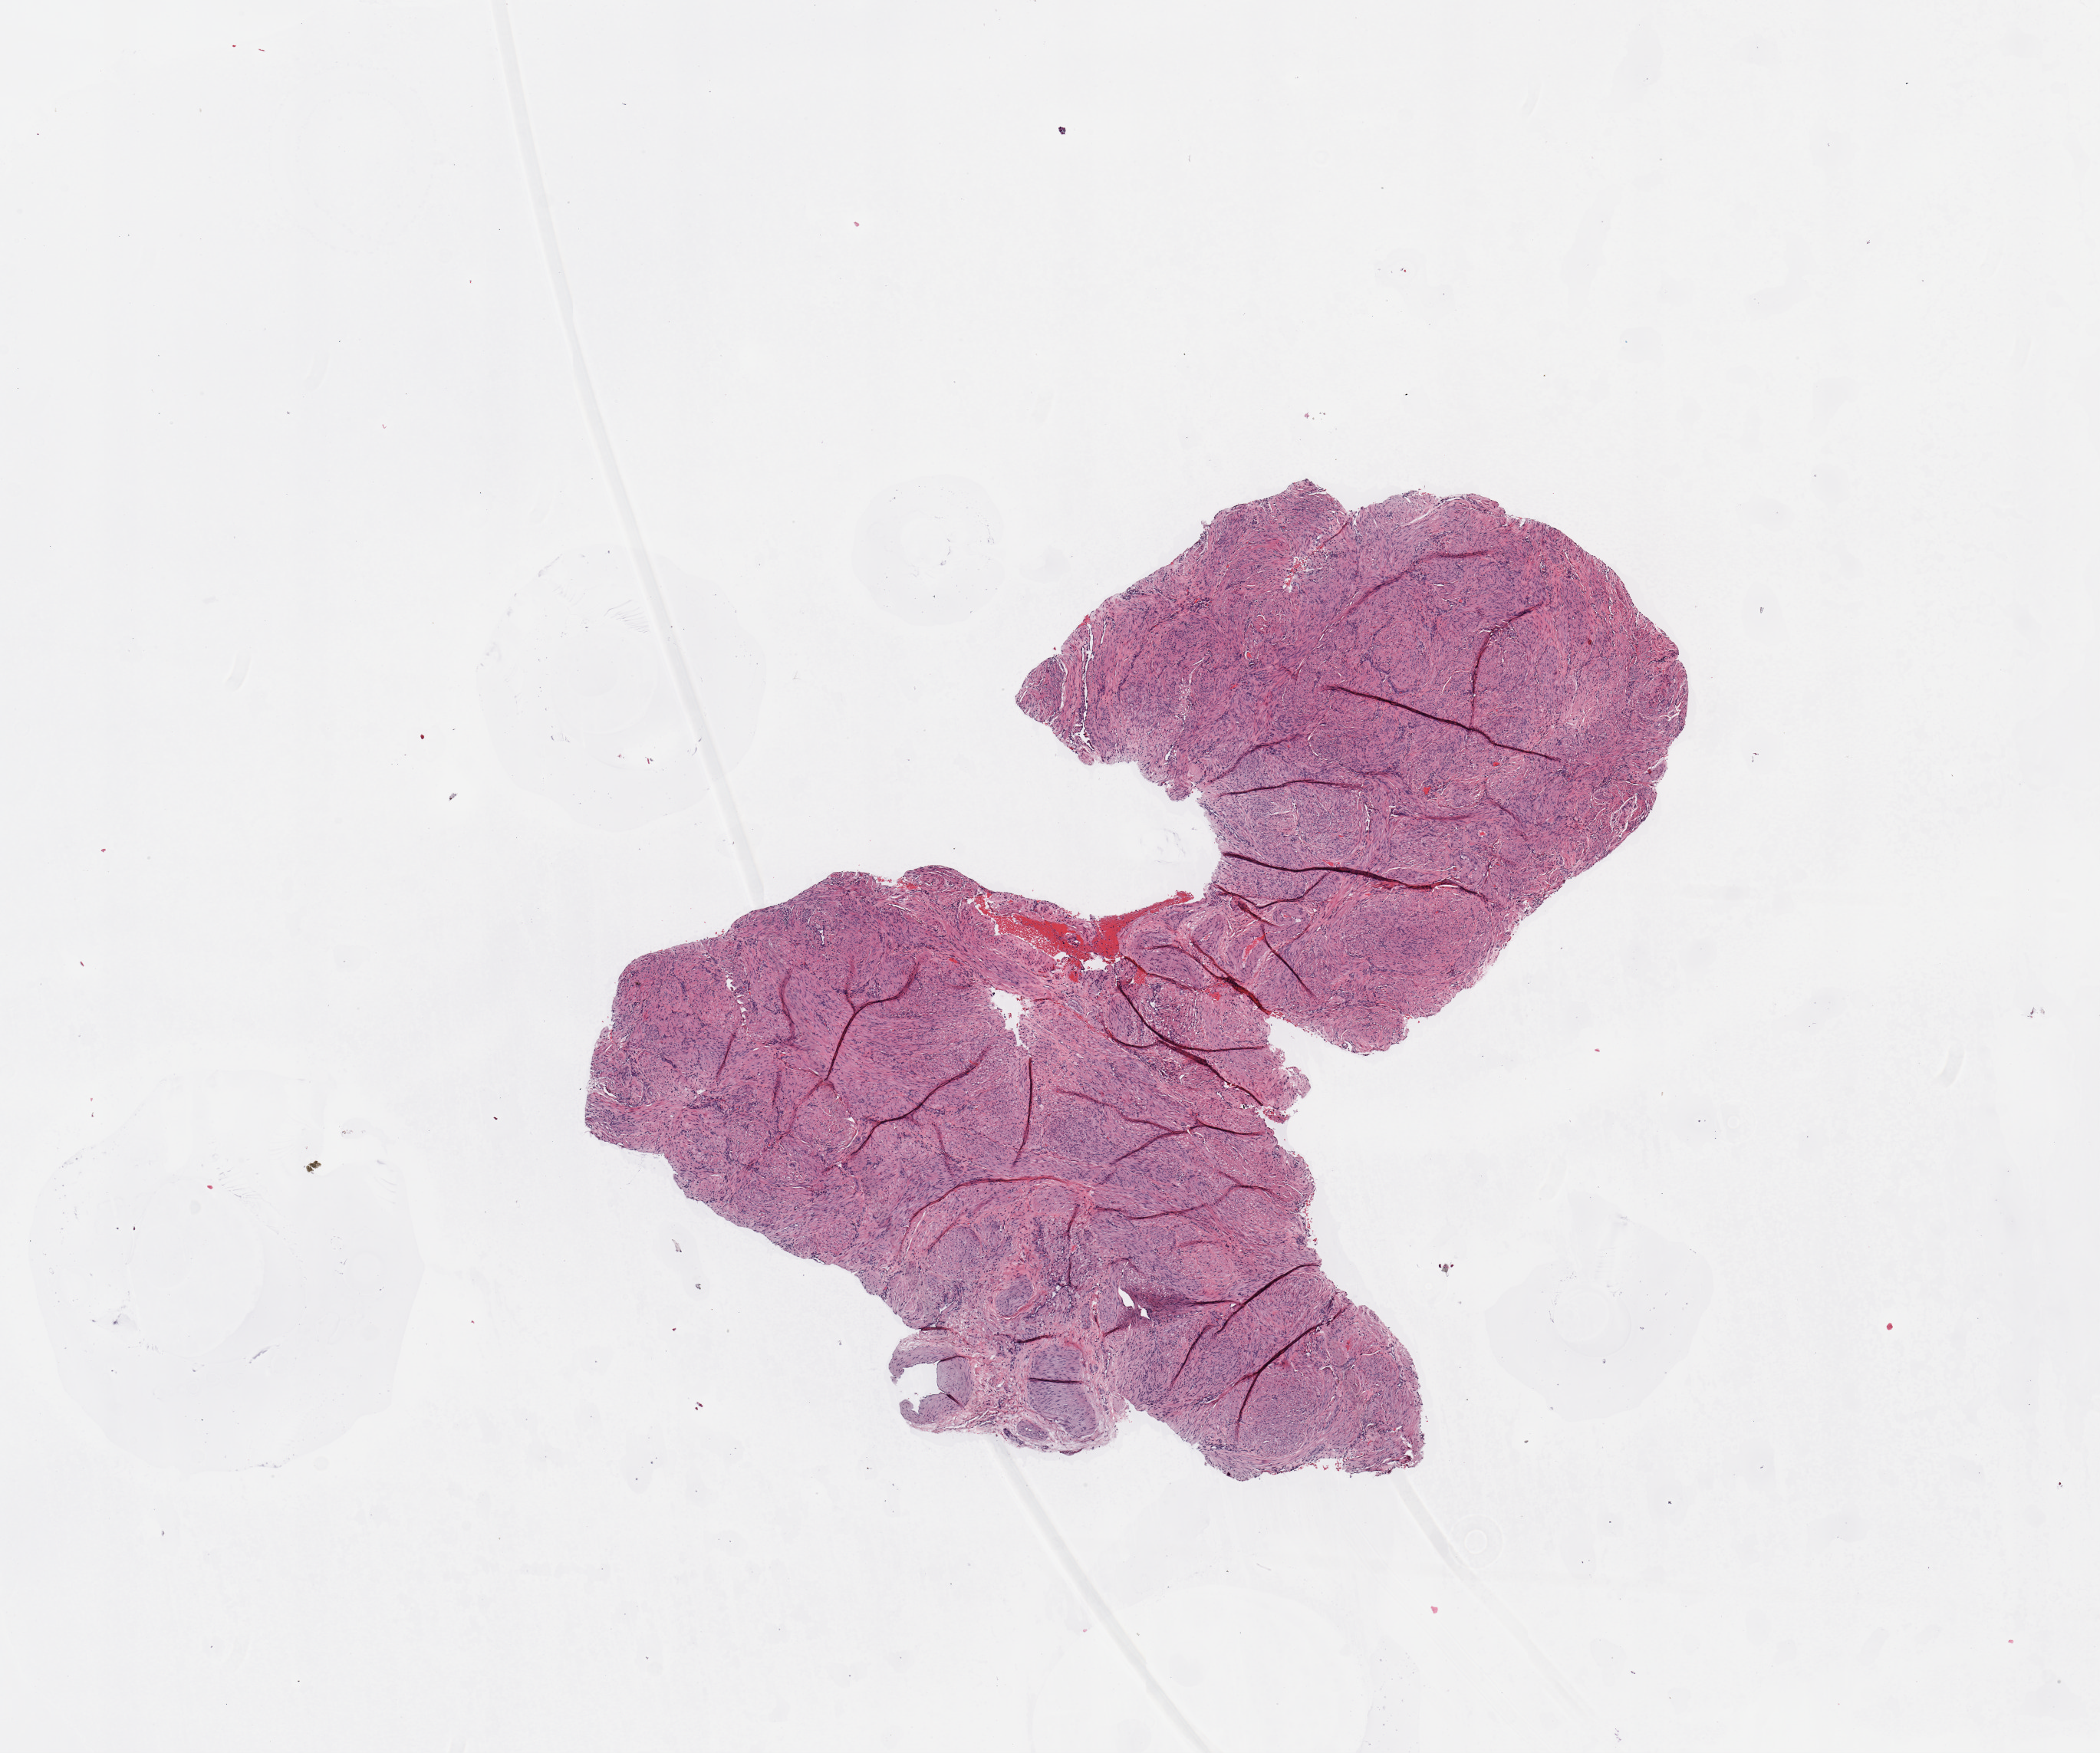
Digitized H&E-stained tissue section (whole slide) — whole scanned area (about 10.8 x 9.0 mm) shown as a low-resolution overview. Normal (non-tumour) tissue sample, uterus. 48-year-old female patient.
This section: normal (non-tumour) tissue from the same patient. Patient diagnosis: Endometrioid adenocarcinoma, NOS.